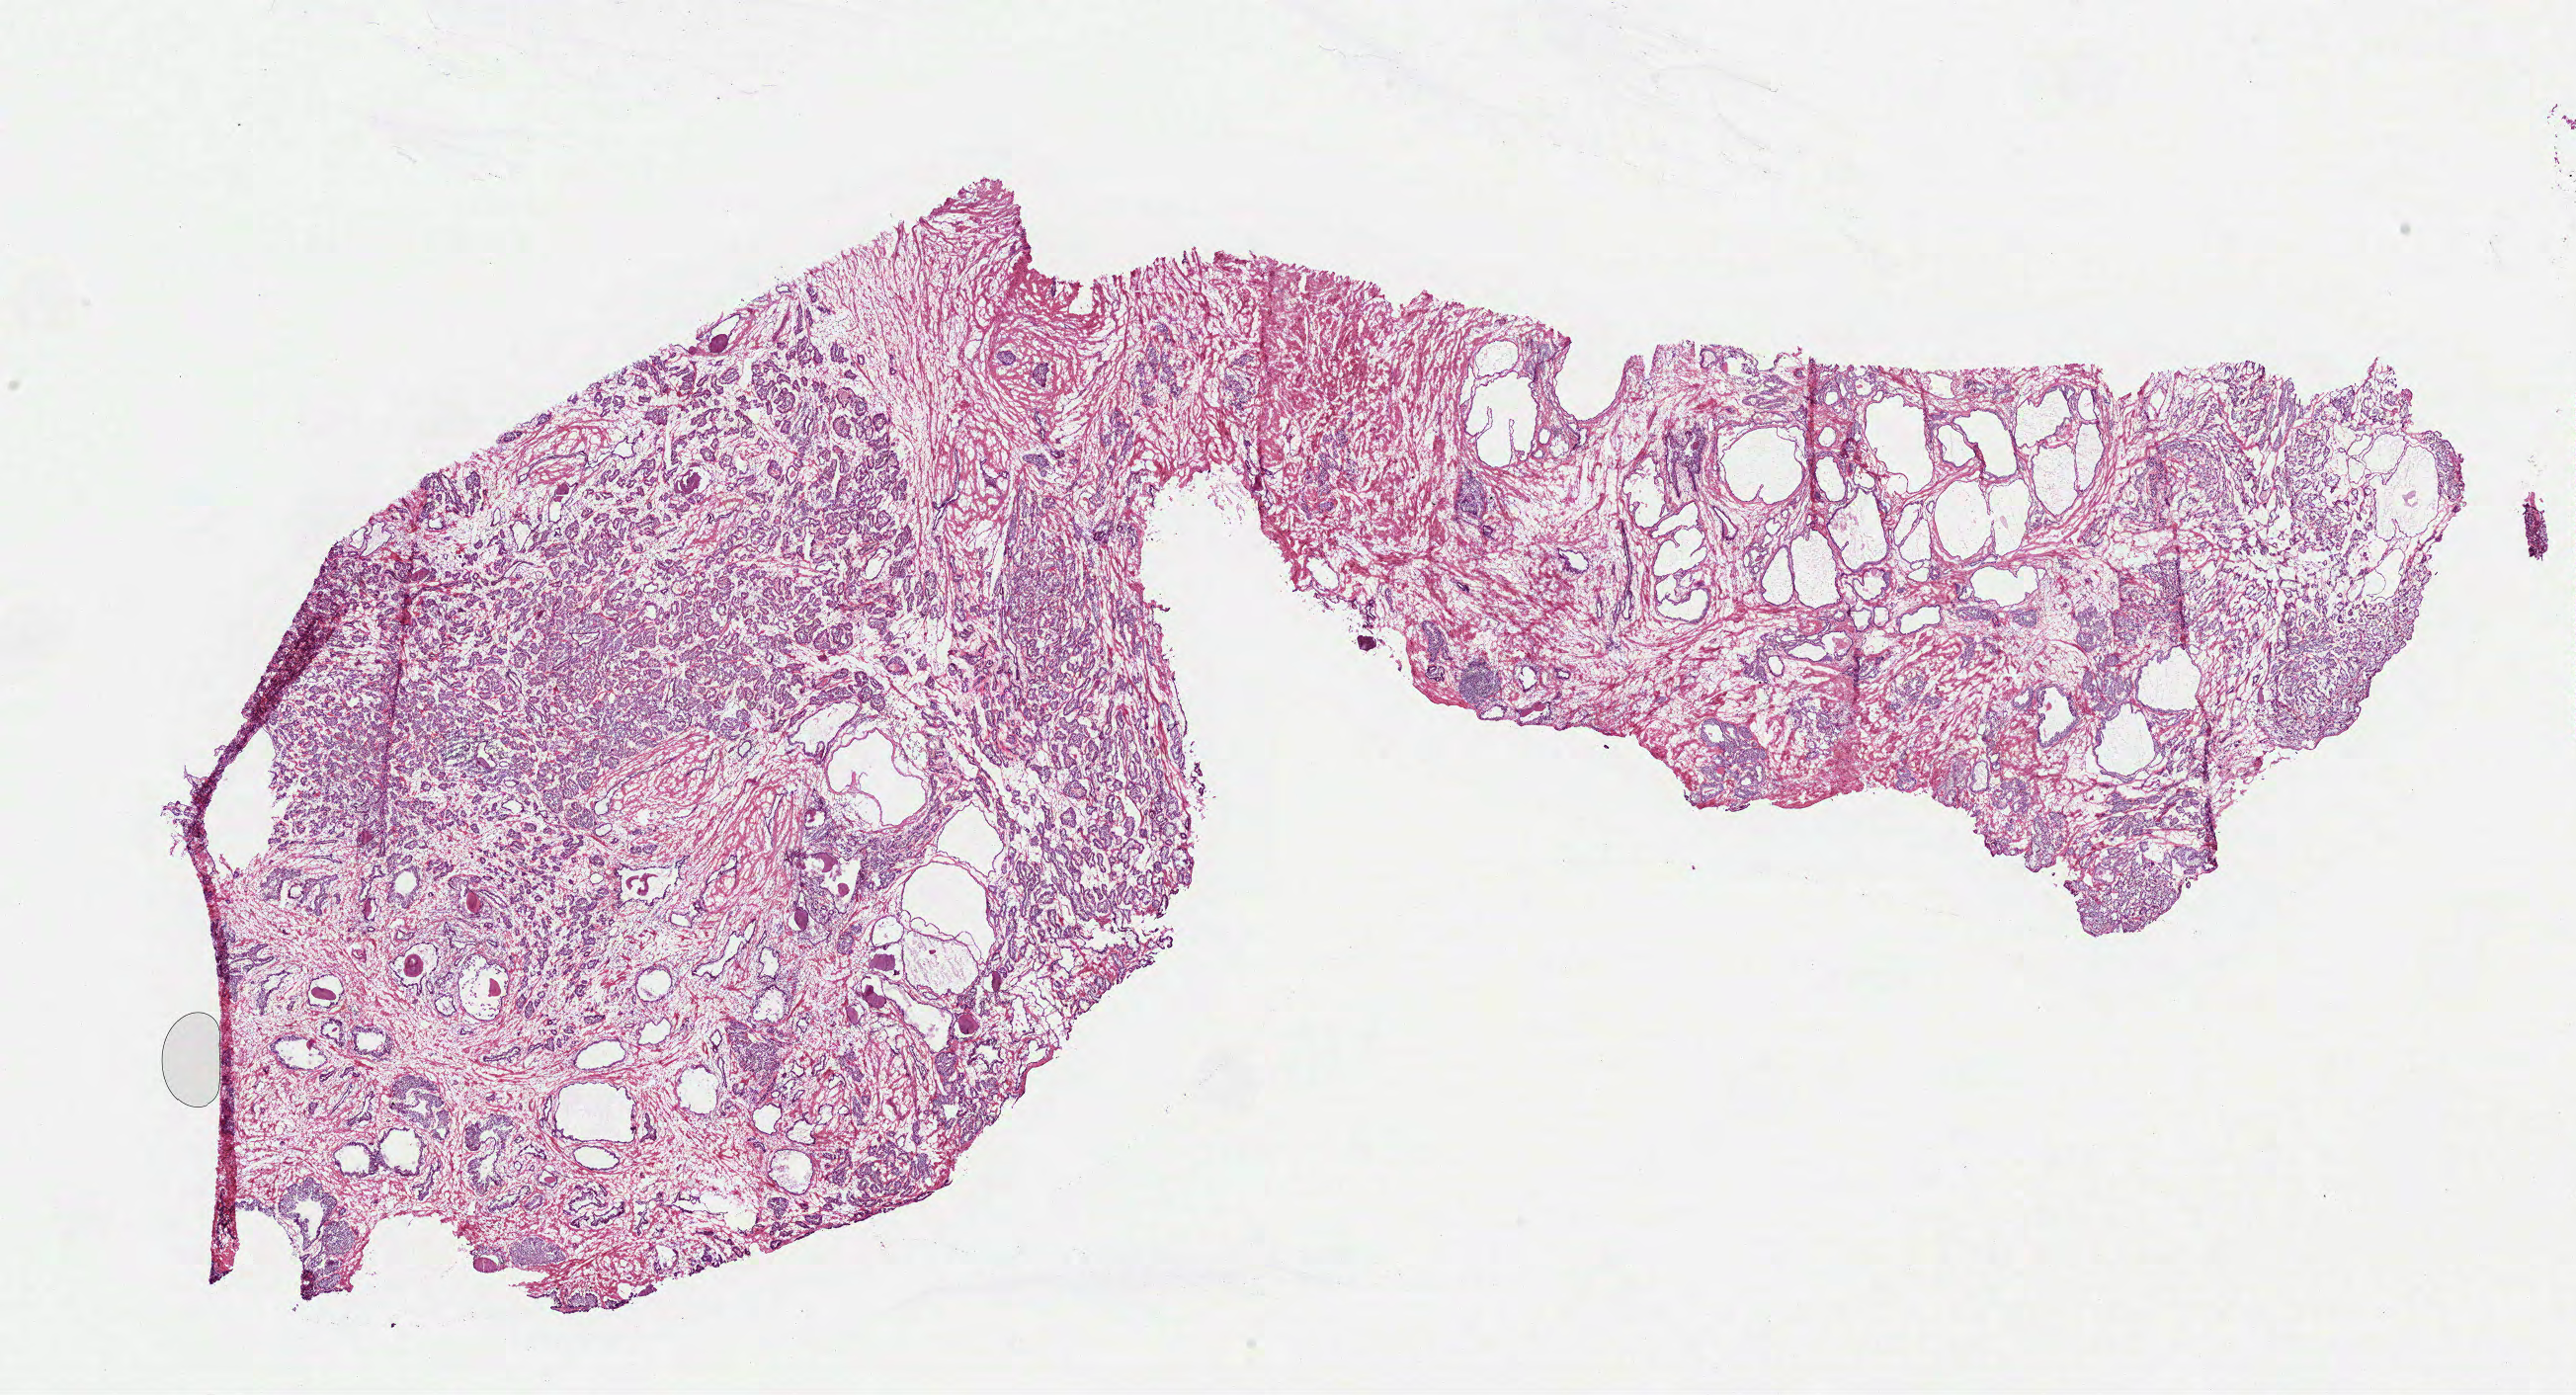
Digitized H&E-stained tissue section (whole slide), whole scanned area (about 21.0 x 11.4 mm) shown as a low-resolution overview. Frozen section from the top of the tissue portion. Prostate, primary tumour sample. Patient: male, age at initial diagnosis 65 years. Gleason score: 7 (3+4). Pathologist review of this section (percent, as recorded): tumour cells 50%, tumour nuclei 70%, normal cells 20%, stromal cells 30%, necrosis 0%. Infiltration values recorded for this section: lymphocyte infiltration 0%, monocyte infiltration 0%, neutrophil infiltration 0%.
Laterality: bilateral. Lymph nodes positive (case pathology): 0 of 17 examined. Pathologic diagnosis: Acinar cell carcinoma.